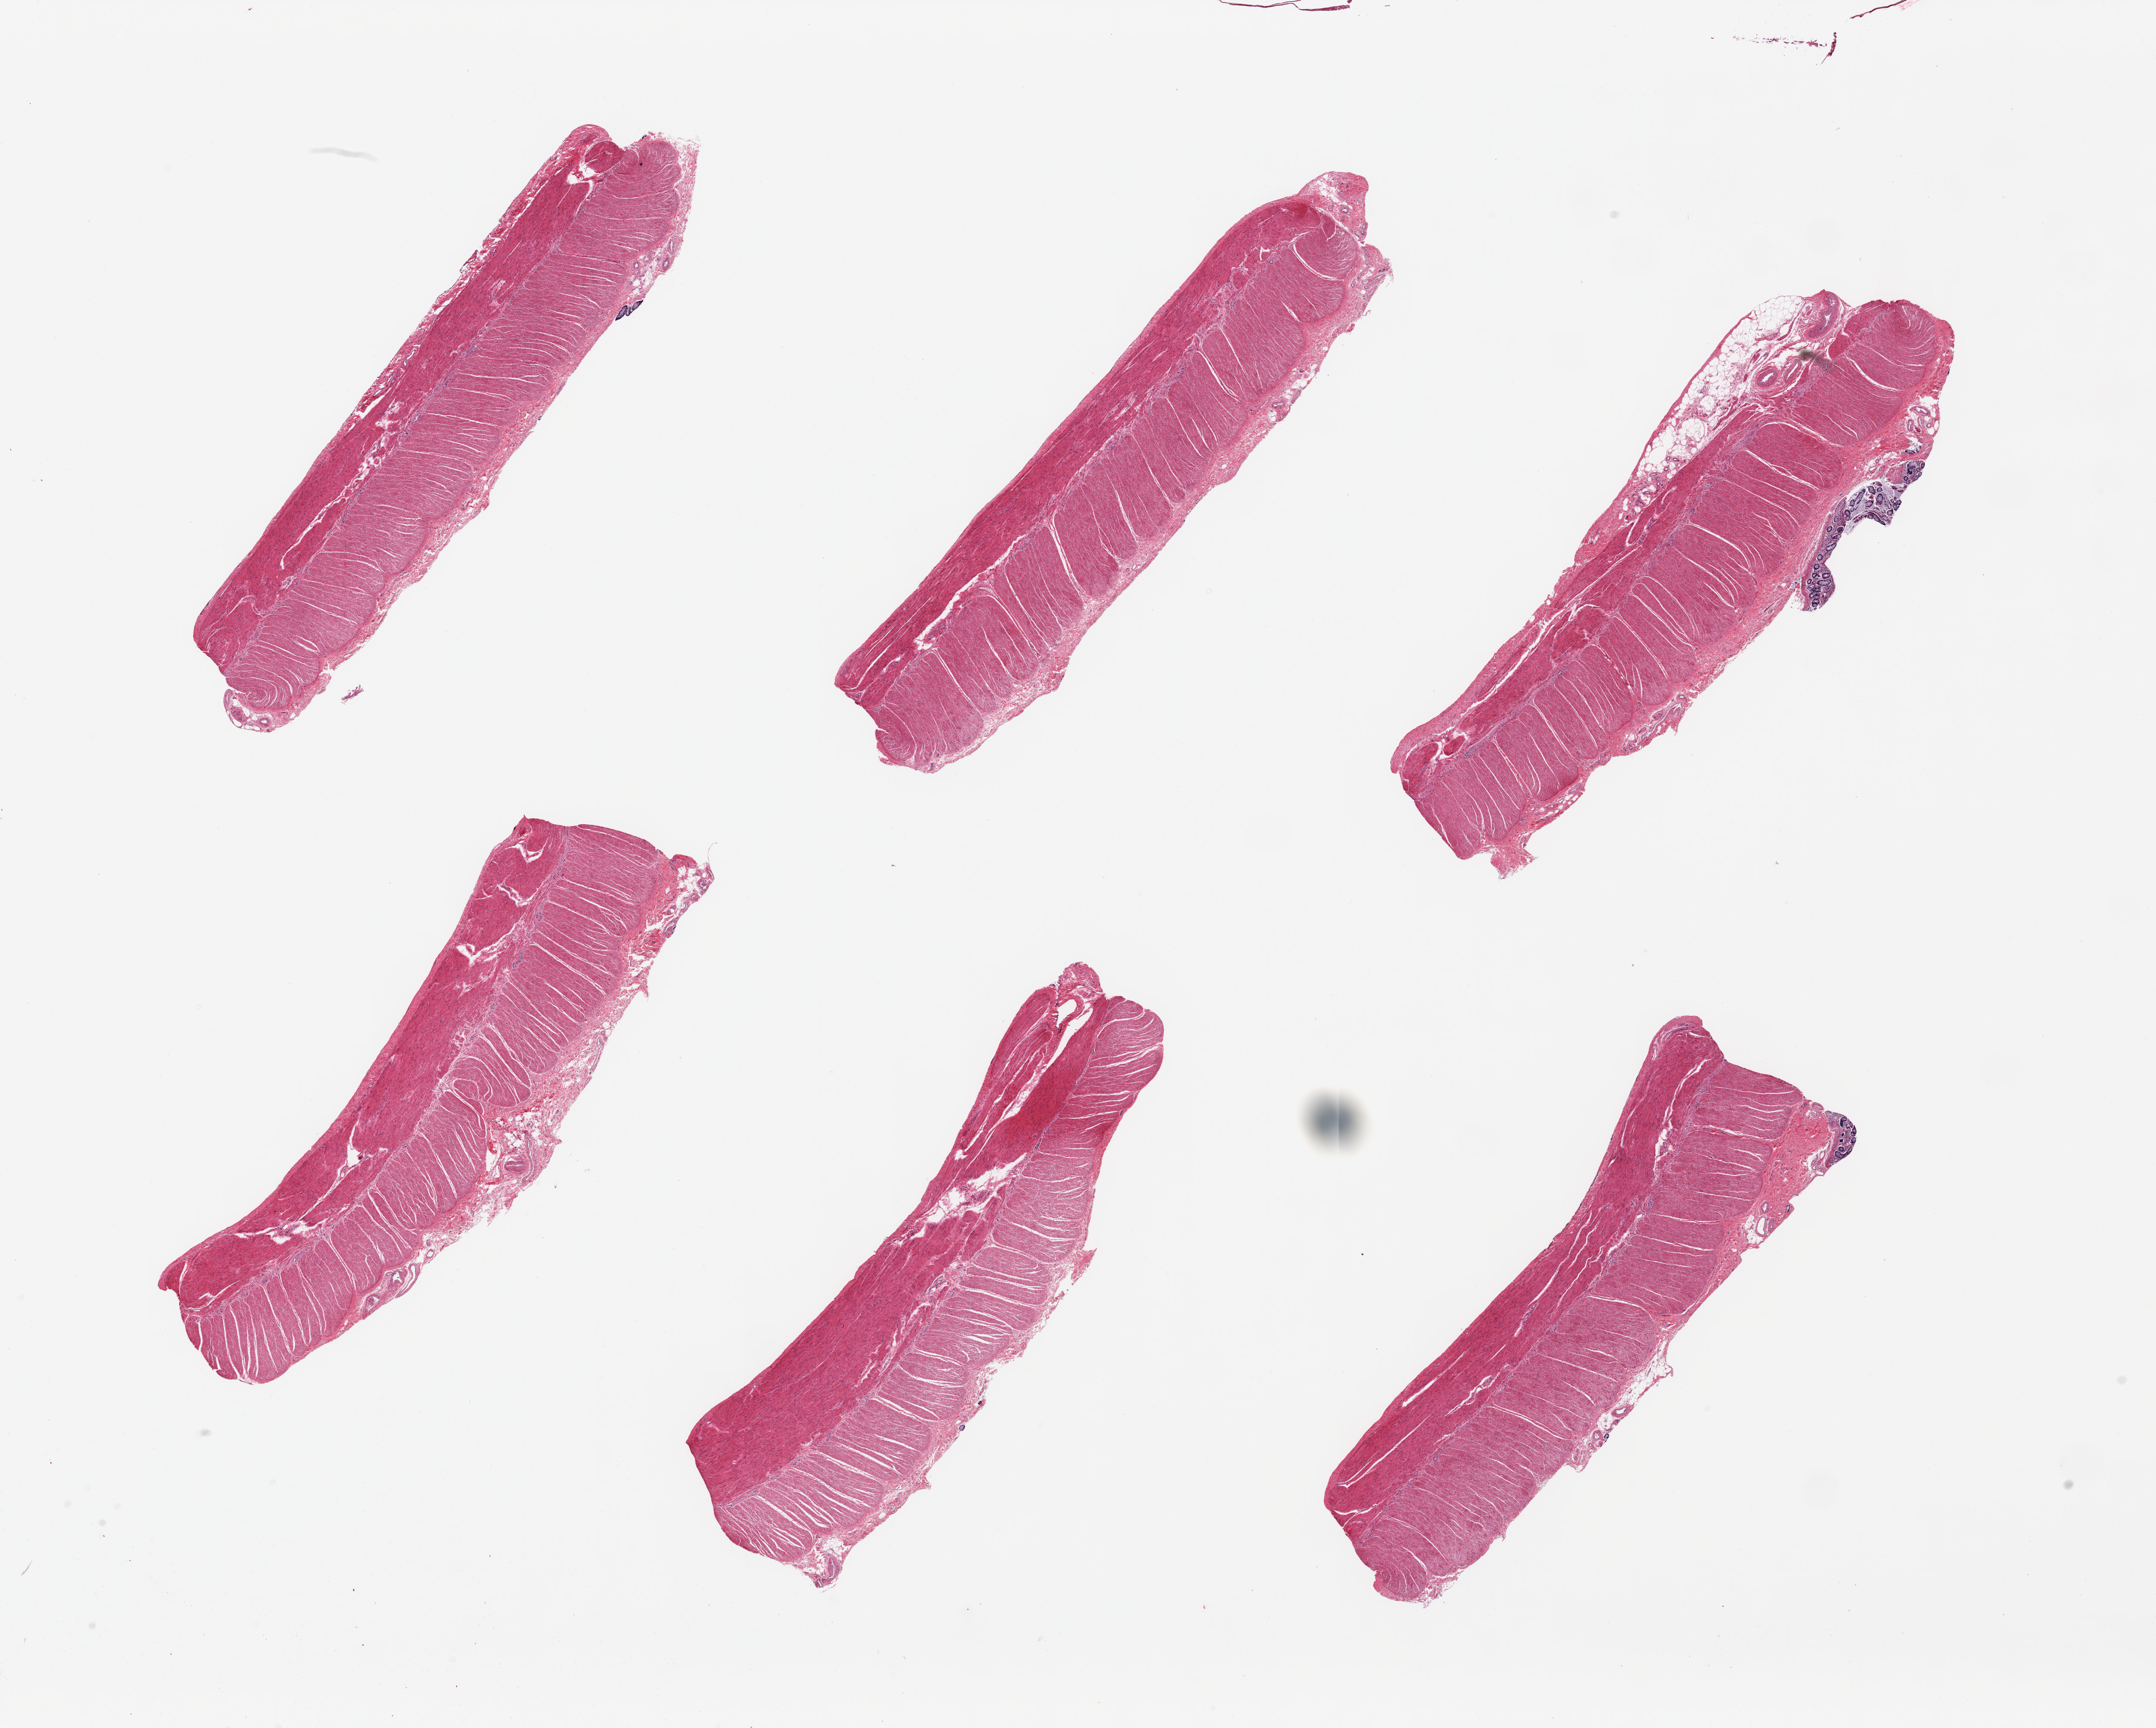
Digitized haematoxylin and eosin-stained section, shown as a low-resolution overview of the whole scanned area (about 28.5 x 22.9 mm, slide scanned at 20x). PAXgene-fixed, paraffin-embedded tissue. Target tissue: sigmoid colon. Tissue donor sample. Male donor.
* reviewer comment on this tissue sample: 6 pieces, confirmed target muscularis